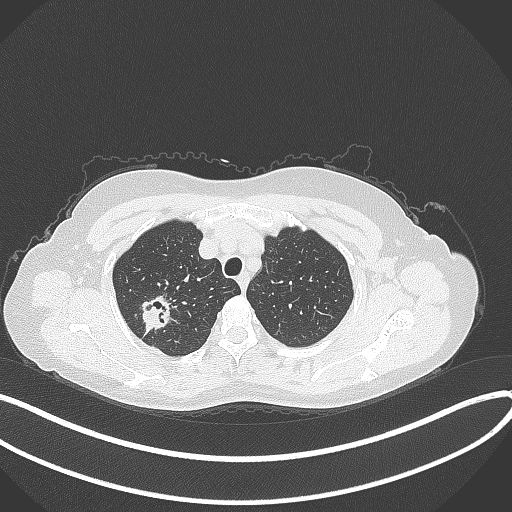
Chest CT, one axial slice. Slice 299 of 337 in the series (ordered by position). Reconstruction kernel B70f. Lung window (W 1500 / L -600 HU). 1 mm slice thickness. 512 × 512 image matrix, field of view 400 × 400 mm. Female patient, age 50 years. From the clinical record (not read from this slice): clinical TNM (as recorded): T1c N0 M0; histopathological grade: G2-3.
Structures marked on this image (bounding box drawn by a radiologist):
- lung tumour (recorded histology: adenocarcinoma): box from (x=136, y=293) to (x=173, y=336) px